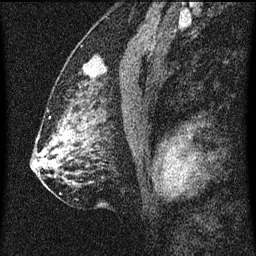
Breast MRI (dynamic contrast-enhanced), one sagittal slice; slice 37 of 60 in the series (ordered by position); dynamic contrast-enhanced series, image 2 of 3 at this slice position (ordered by acquisition); 1.5 T; TE 4.2 ms, TR 8 ms; 2 mm slice thickness; 256 × 256 image matrix, field of view 180 × 180 mm. Female patient, age 52 years.
Structures marked on this image (semi-automatic segmentation, software-assisted and operator-edited):
- analysis volume of interest (the breast-tissue region the enhancement analysis was run in; not a lesion): bounding box <72,52,116,101> (left, top, right, bottom; pixels)
- tumour enhancement mask (voxels above the 70 % enhancement threshold inside the analysis volume of interest): <84,66,88,73>